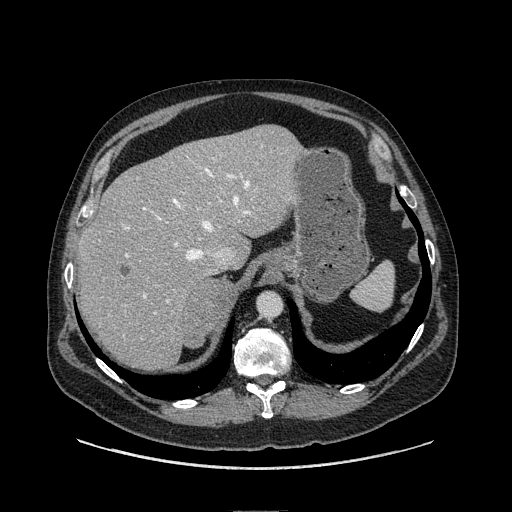
Contrast-enhanced abdominal CT, one axial slice. Soft-tissue window (W 400 / L 40 HU). 512 × 512 image matrix, field of view 440 × 440 mm. Male patient. Case-level facts recorded for this patient, not image findings: diagnosis: adrenocortical carcinoma; tumour side: right adrenal; tumour size at pathology: 7.5 cm; Ki-67 index: 15 %; stage (as recorded): 2.
Outlined on this slice (semi-automatically segmented with operator editing):
- mass: bounding box (x1, y1, x2, y2) in pixels: (185, 277, 230, 346)